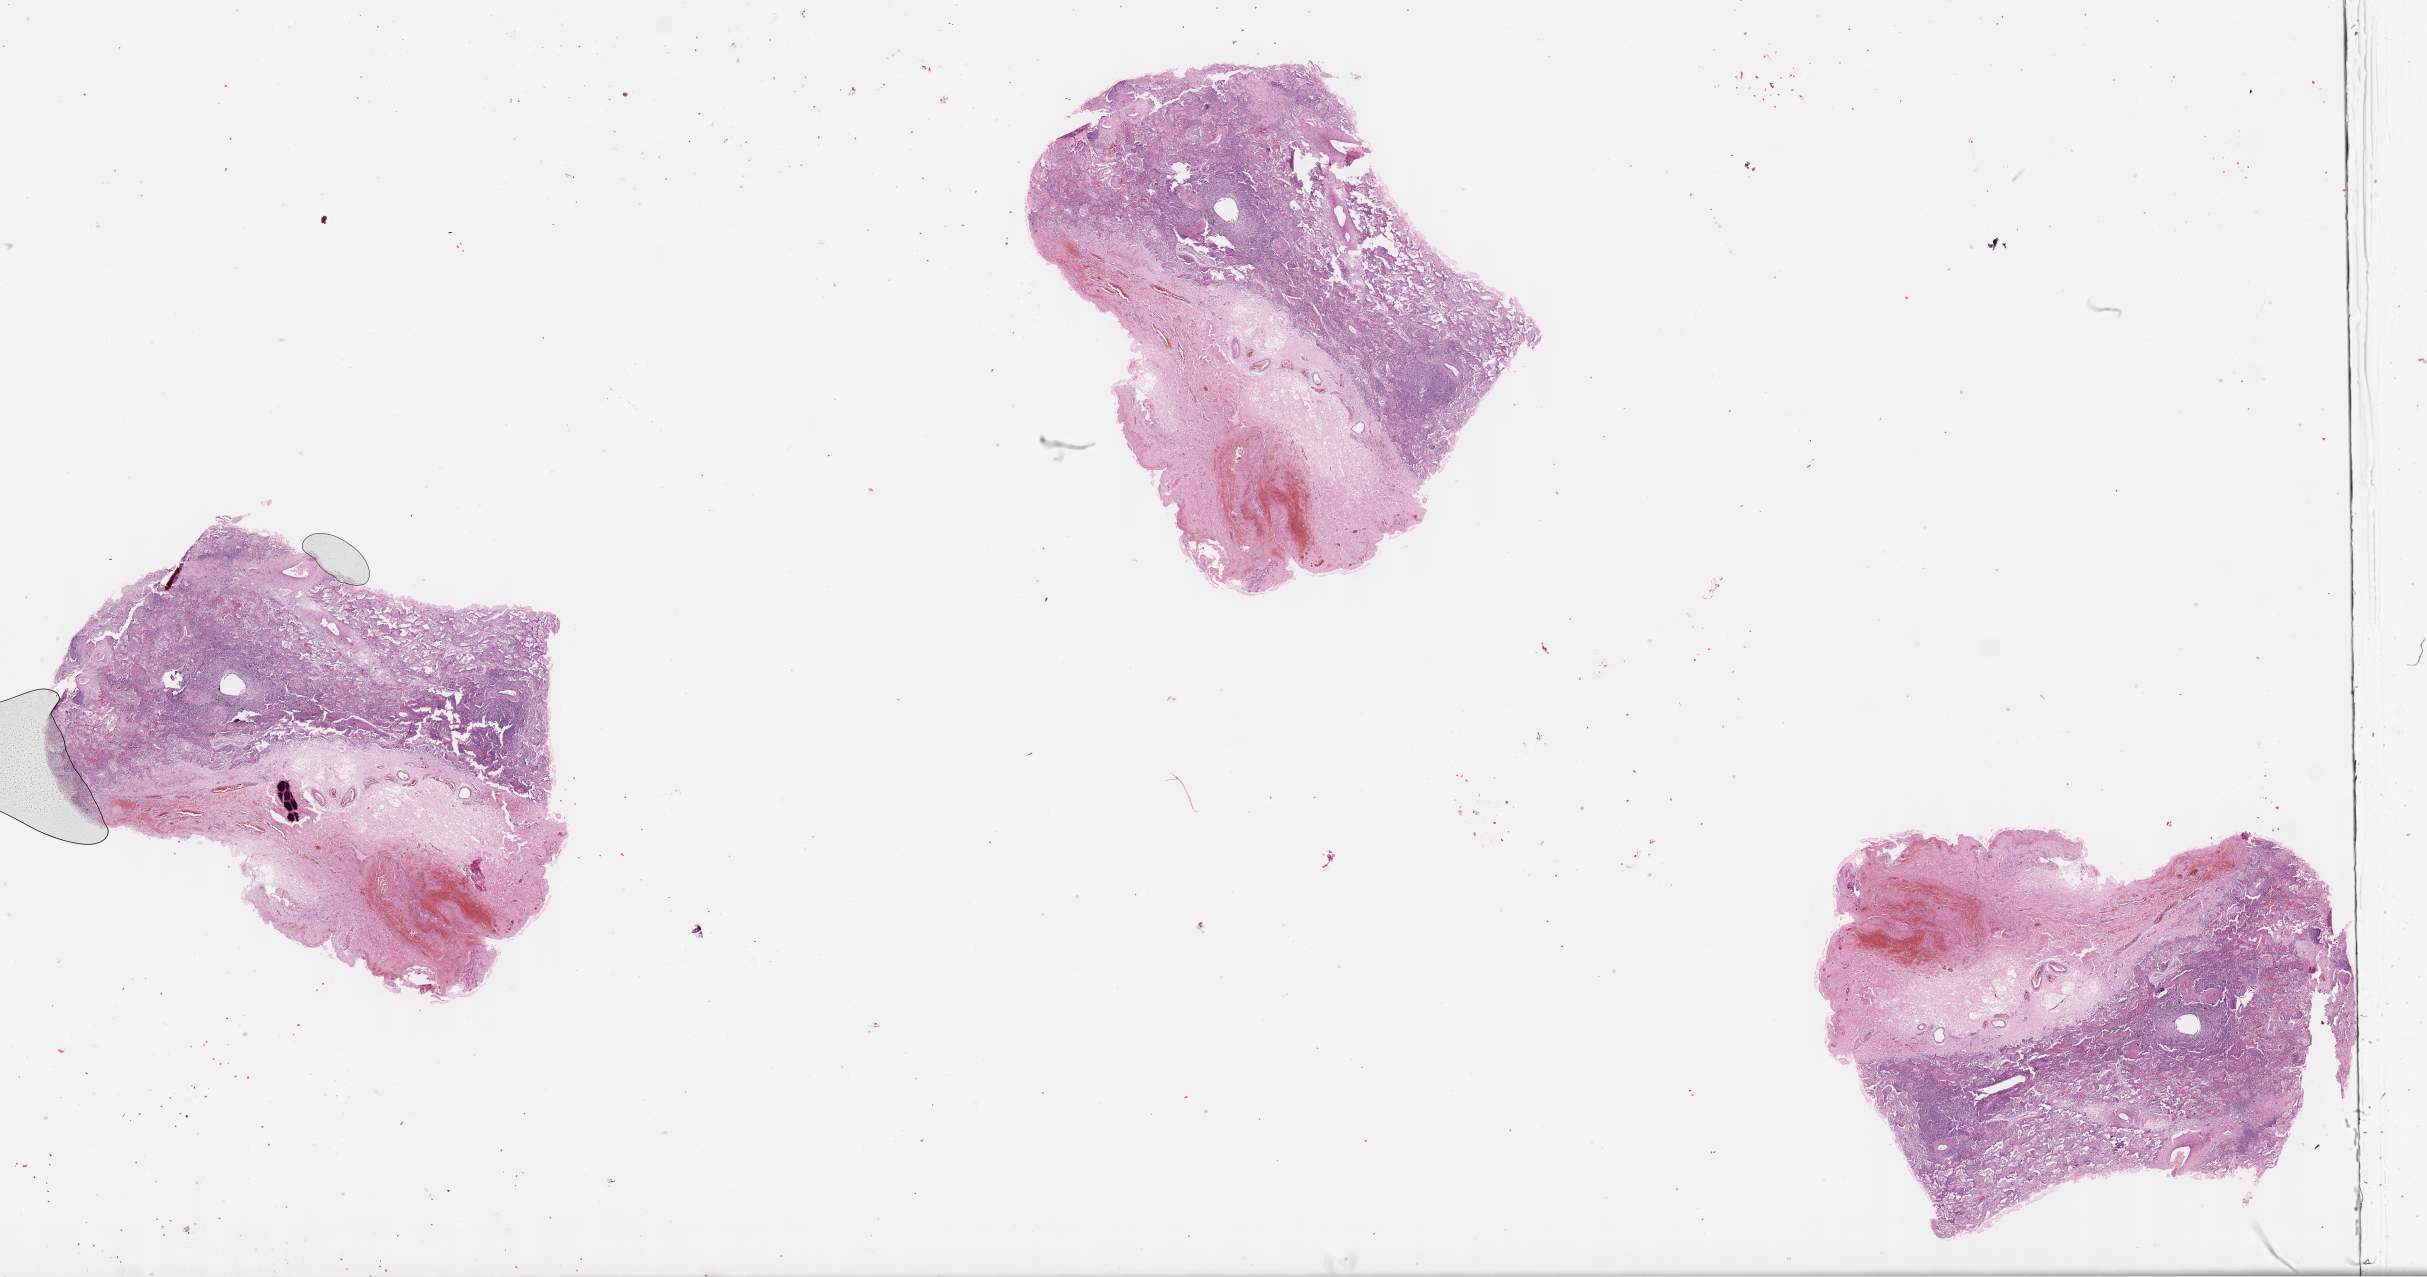
Whole-slide histology image, H&E-stained — shown as a low-resolution overview of the whole scanned area (about 39.1 x 20.6 mm, slide scanned at 20x), lung, normal (non-tumour) tissue. Male, 59 y/o.
This section: normal (non-tumour) tissue from the same patient. Patient diagnosis (cohort enrolment): squamous cell carcinoma (lung).